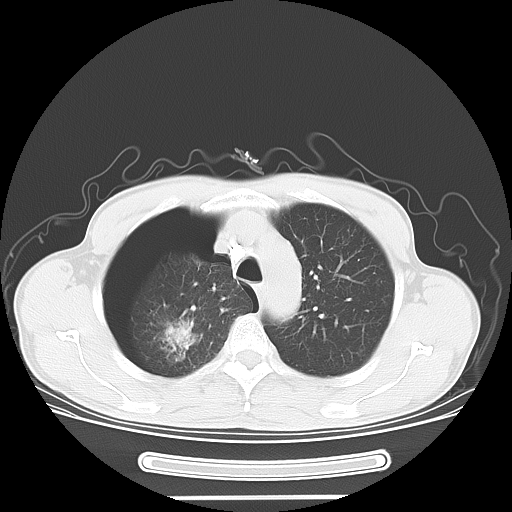
Chest CT, one axial slice. Position 52 of 67 along the scan axis. Reconstruction kernel LUNG. Lung window (W 1500 / L -600 HU). 5 mm slice thickness. 512 × 512 image matrix, field of view 375 × 375 mm. Male patient. Case-level facts recorded for this patient, not image findings: clinical TNM (as recorded): T1c N0 M0.
Outlined on this slice (rectangle marked by the reading radiologist):
- lung tumour (recorded histology: adenocarcinoma): box from (x=163, y=315) to (x=196, y=360) px